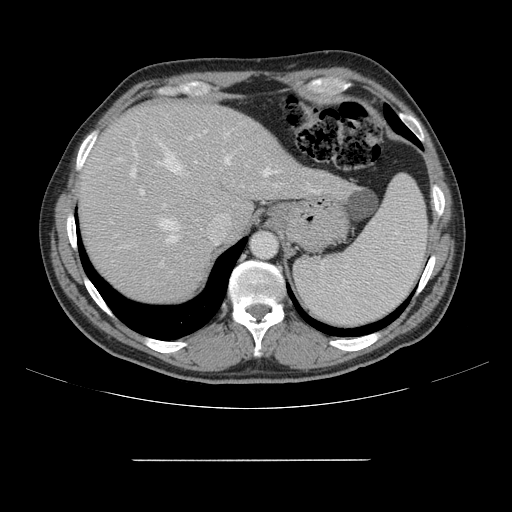
Contrast-enhanced abdominal CT, one axial slice; position 119 of 164 along the scan axis; intravenous contrast given; soft-tissue window (W 400 / L 40 HU); 2.5 mm slice thickness; 512 × 512 image matrix. Male patient, age 54 years. Case-level facts recorded for this patient, not image findings: diagnosis: colorectal cancer liver metastases, imaged before liver resection; multiple liver metastases: yes; largest metastasis: 1 cm.
Structures marked on this image (outlined manually by an expert reader):
- hepatic veins: box from (x=160, y=144) to (x=272, y=243) px
- liver: (x=79, y=104)–(x=347, y=301)
- planned liver remnant (the part of the liver to remain after resection): (x=79, y=104)–(x=251, y=301)
- portal vein (with intrahepatic branches): (x=118, y=137)–(x=277, y=273)